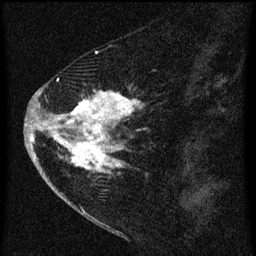
Breast MRI (dynamic contrast-enhanced), one sagittal slice; position 23 of 60 along the scan axis; dynamic contrast-enhanced series, image 2 of 3 at this slice position (ordered by acquisition); 1.5 T; TE 4.2 ms, TR 8 ms; 256 × 256 image matrix, field of view 180 × 180 mm. Patient: female, 47 years.
Structures marked on this image (semi-automatically segmented with operator editing):
- analysis volume of interest (the breast-tissue region the enhancement analysis was run in; not a lesion): bounding box (x1, y1, x2, y2) in pixels: (38, 76, 151, 193)
- tumour enhancement mask (voxels above the 70 % enhancement threshold inside the analysis volume of interest): (39, 78, 145, 175)